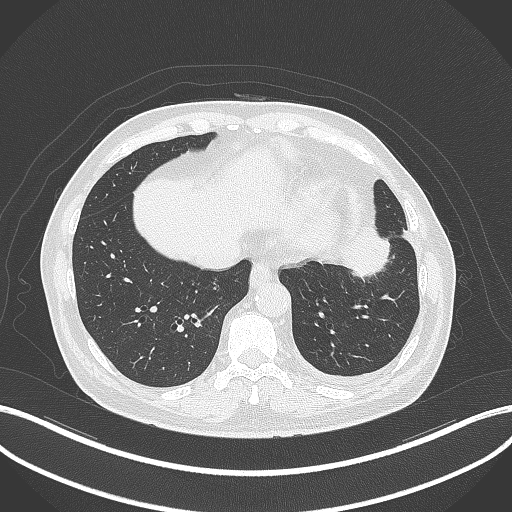
Chest CT, one axial slice. Slice 92 of 230 in the series (ordered by position). 120 kVp. Lung window (W 1500 / L -600 HU). 1 mm slice thickness. 512 × 512 image matrix, field of view 400 × 400 mm. Male patient, age 68 years. Case-level facts recorded for this patient, not image findings: clinical TNM (as recorded): T2b N0 M0.
Outlined on this slice (bounding box drawn by a radiologist):
- lung tumour (recorded histology: squamous cell carcinoma): bounding box <337,224,400,285> (left, top, right, bottom; pixels)